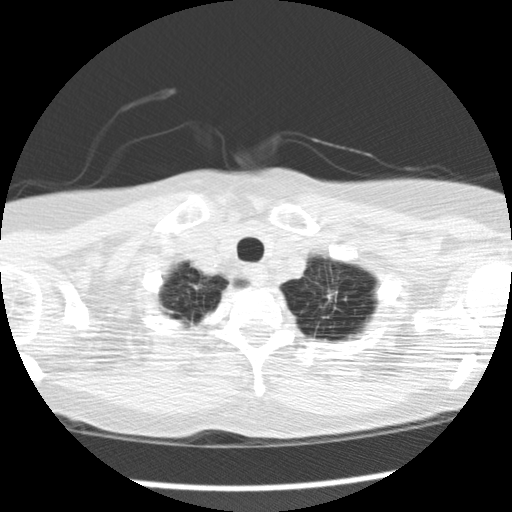
Low-dose screening chest CT, one axial slice; slice 148 of 159 in the series (ordered by position); reconstruction kernel STANDARD; lung window (W 1500 / L -600 HU); 2.5 mm slice thickness; 512 × 512 image matrix.
Structures marked on this image (outlined manually by an expert reader):
- lesion 1 (tumor, upper lobe of left lung): bounding box <327,292,336,301> (left, top, right, bottom; pixels)